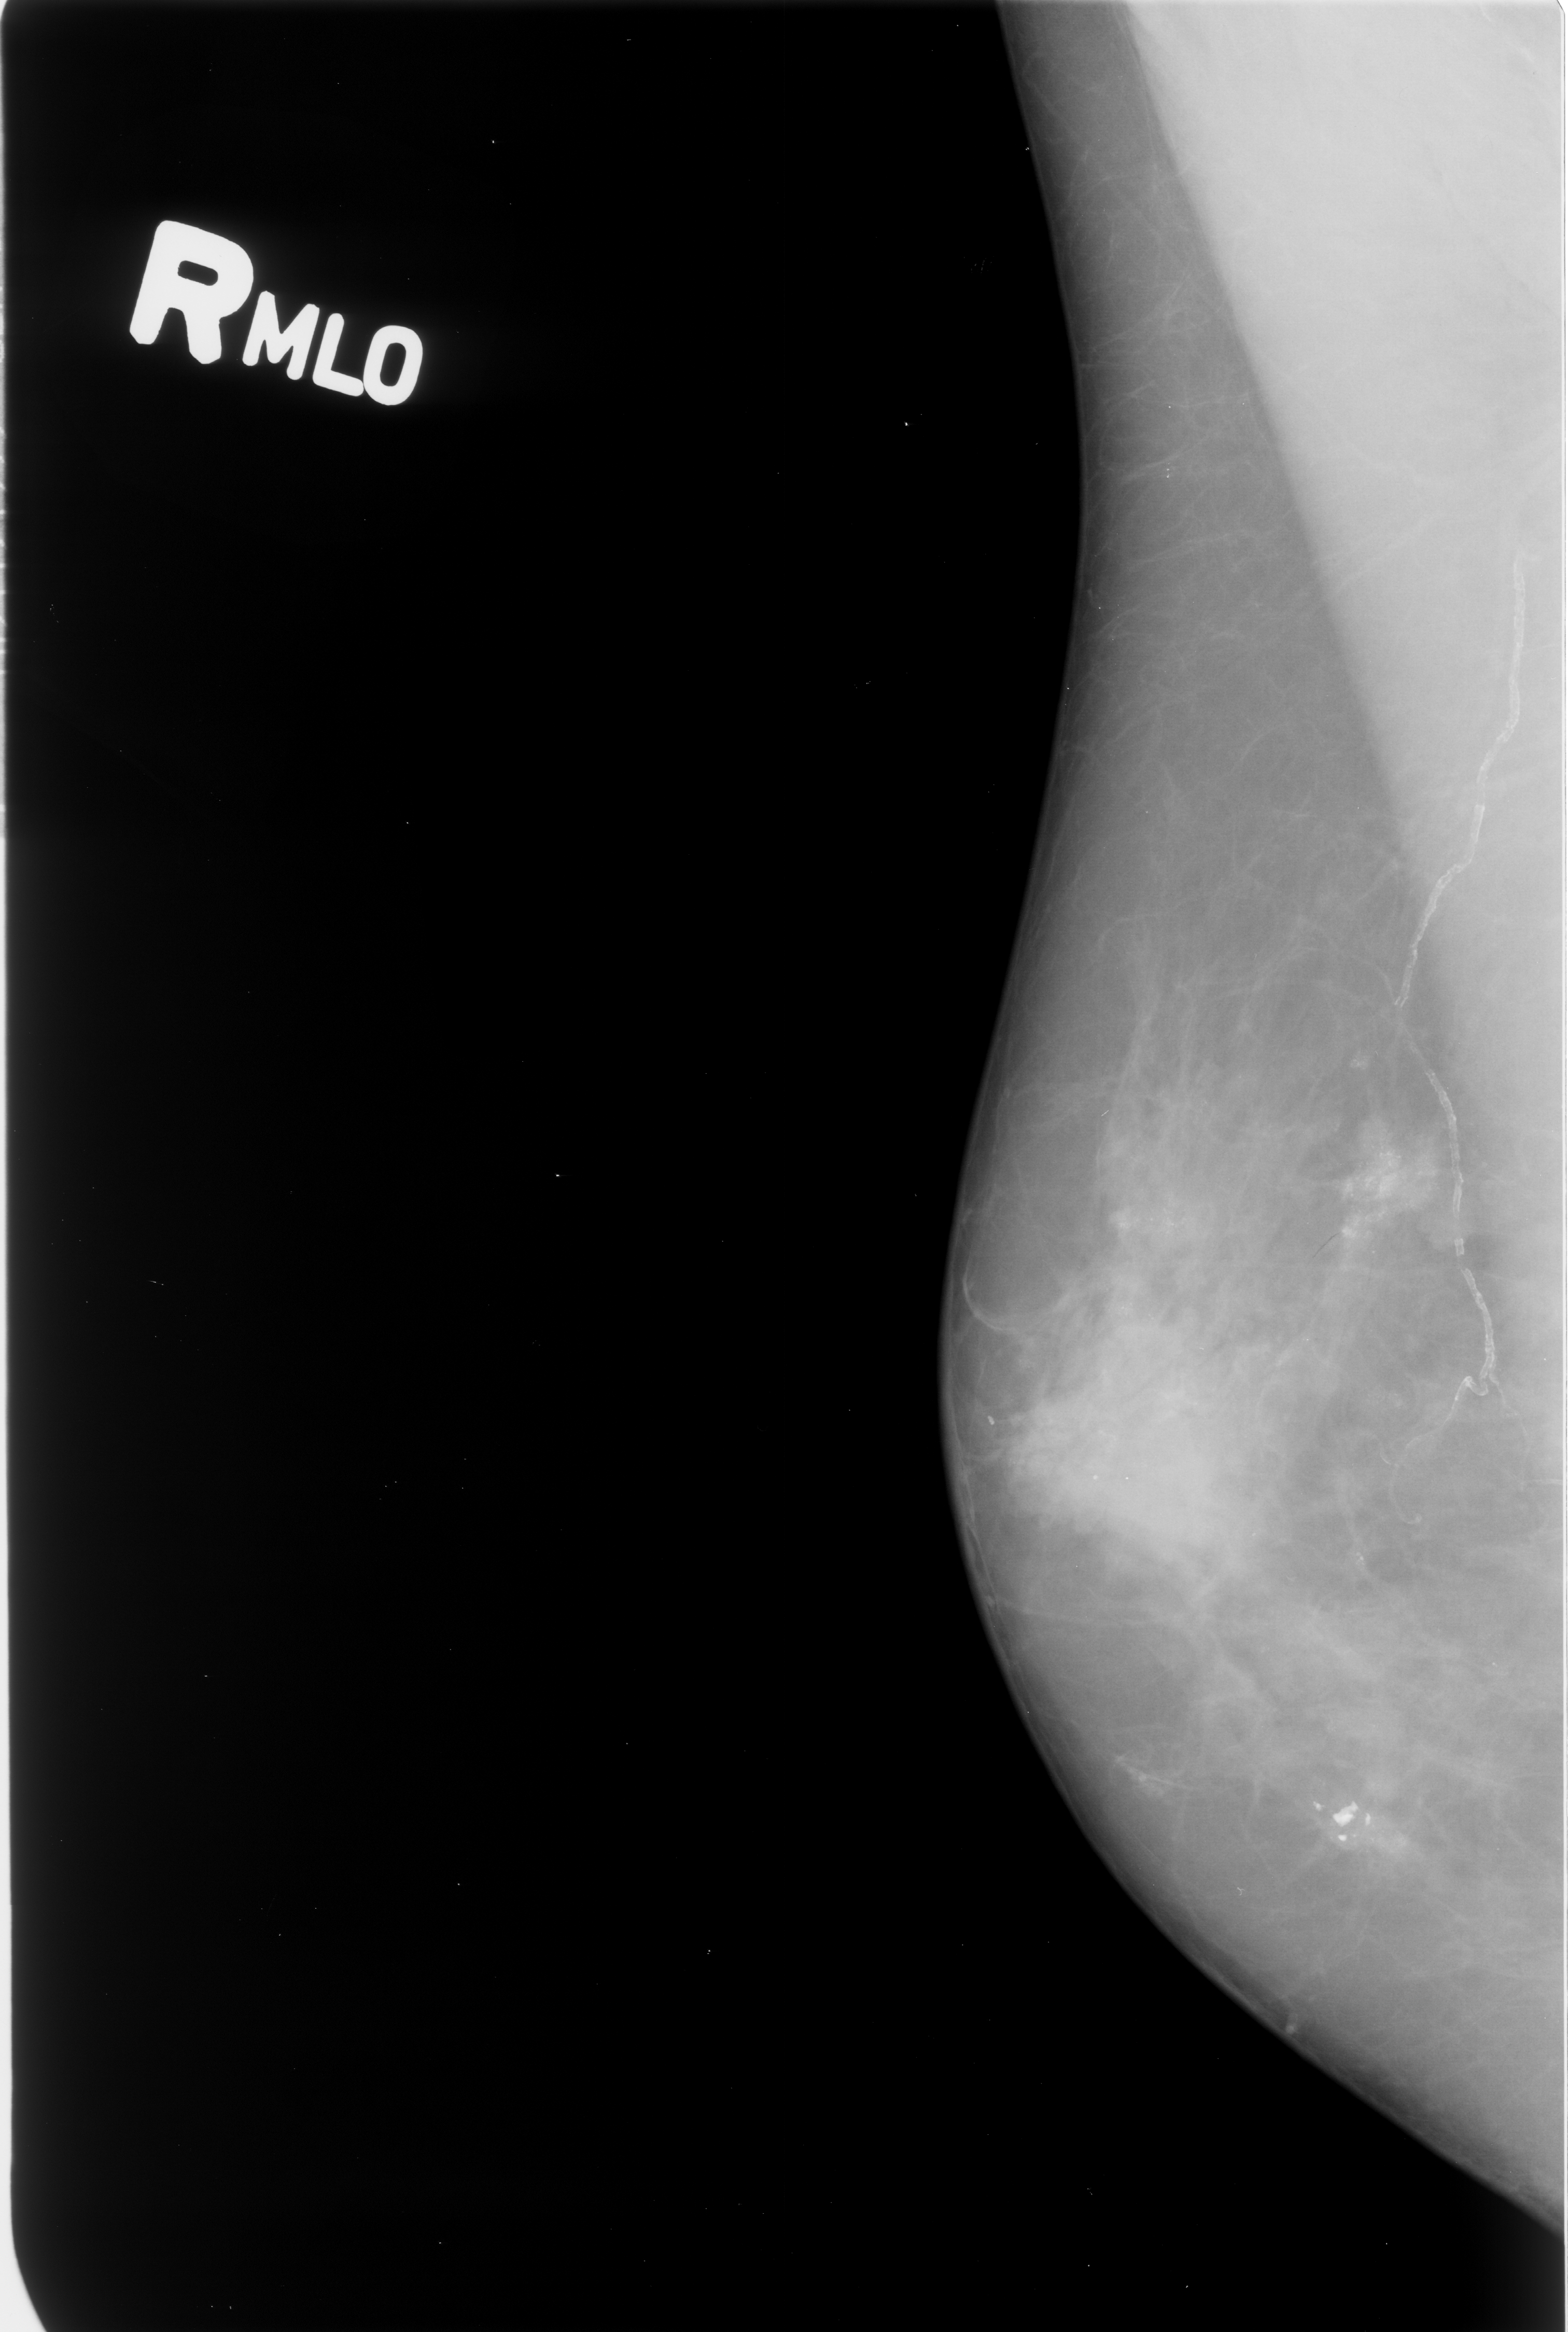
Digitized screen-film mammogram. Right breast. MLO view. BI-RADS breast density category 3 (scale 1–4). 1568 × 2332 image matrix.
Expert-marked regions of interest on this film, with their recorded descriptors:
- calcifications, morphology punctate / pleomorphic, distribution clustered; BI-RADS assessment category 4; pathology result (as recorded, not read from the image): malignant: bounding box (x1, y1, x2, y2) in pixels: (1302, 1087, 1503, 1312)